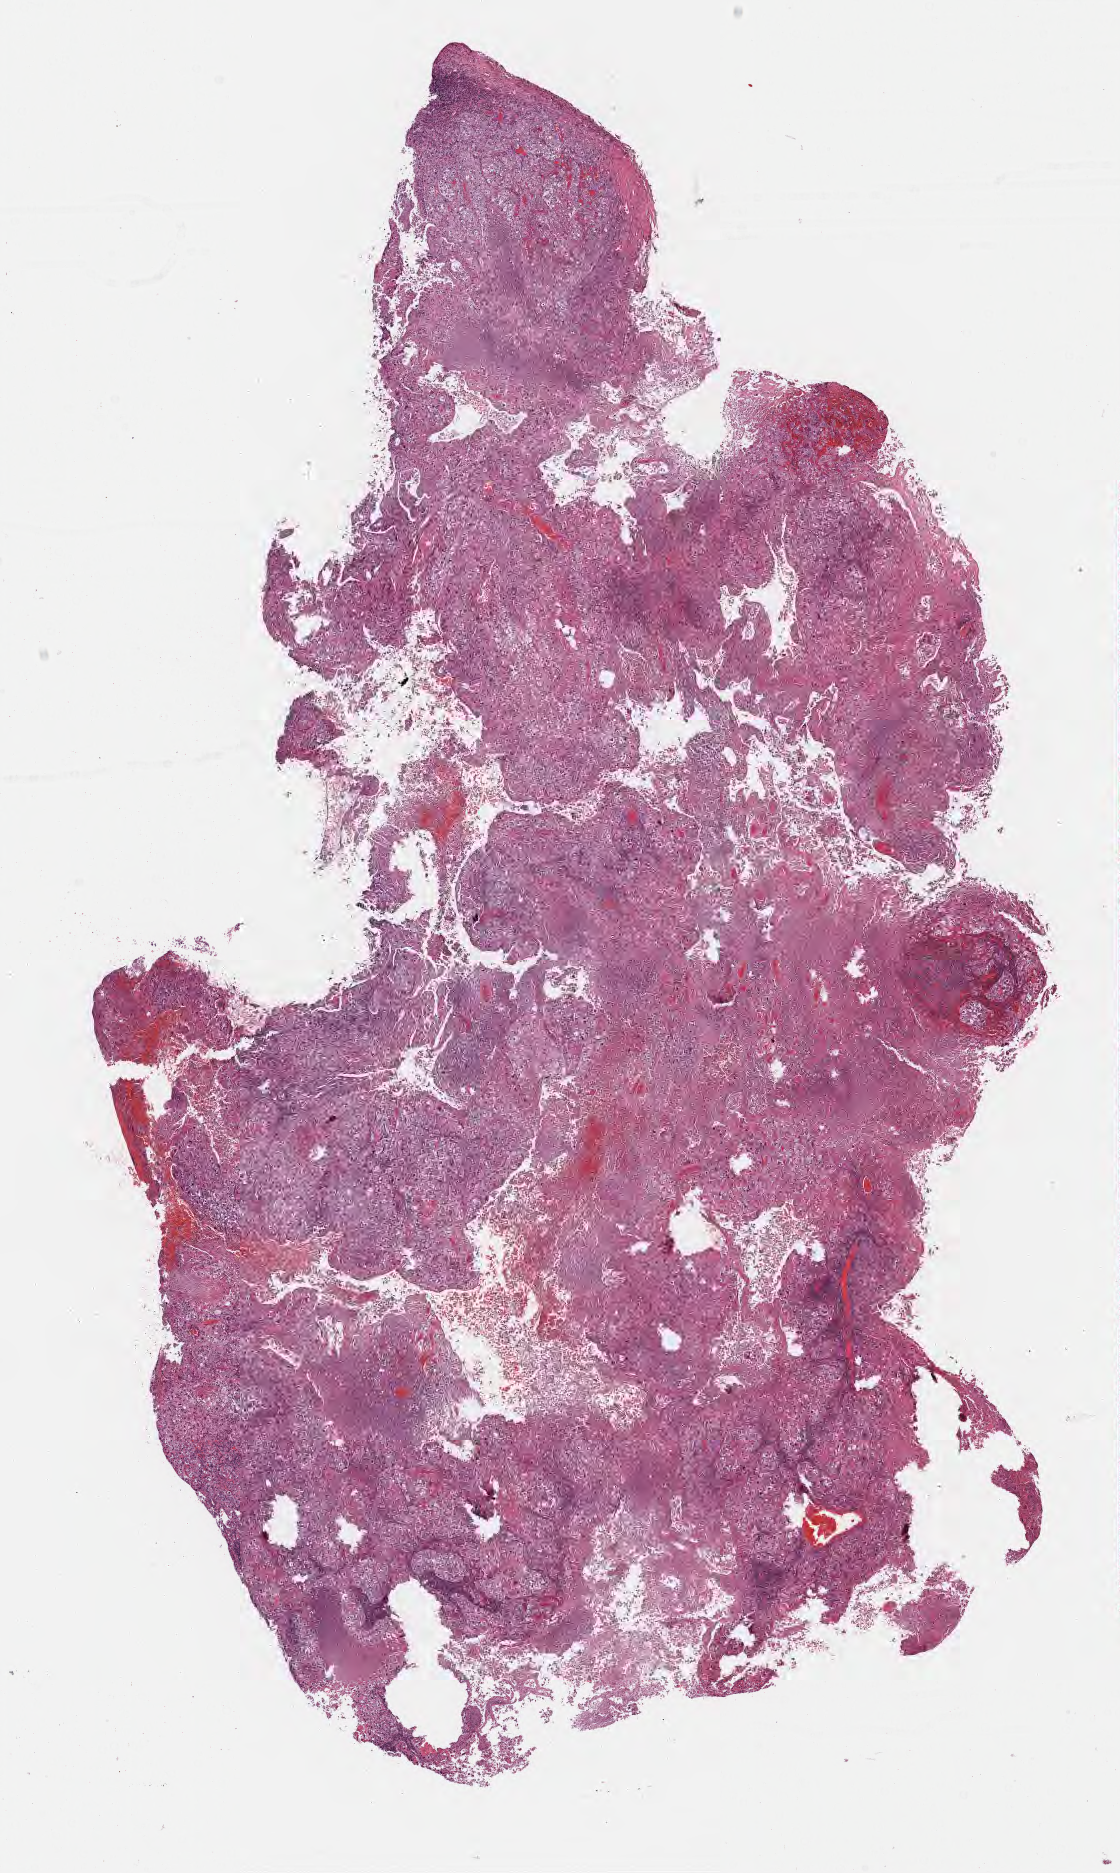
Hematoxylin and eosin (H&E) whole-slide image — low-resolution overview of the scanned area, about 9.1 x 15.2 mm. Patient sex: female.
Specimen: tumor tissue; anatomic site: lower respiratory tract.